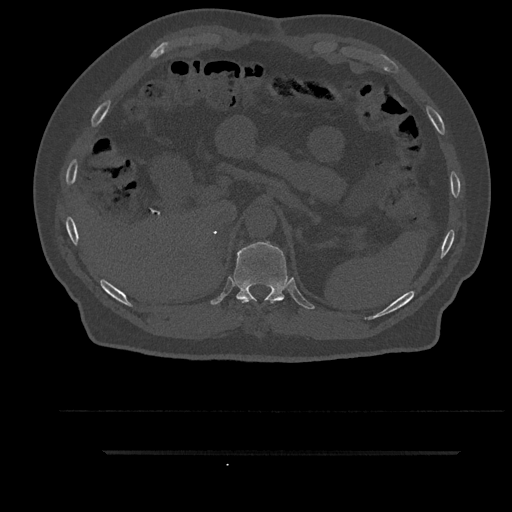
CT including the spine, one axial slice; position 326 of 797 along the scan axis; reconstruction kernel Br40s/3; 120 kVp; bone window (W 1800 / L 400 HU); 512 × 512 image matrix, field of view 432 × 432 mm. Male patient, age 63 years. From the clinical record (not read from this slice): primary cancer: renal.
Structures marked on this image (semi-automatically segmented with operator editing):
- T10 vertebra: bounding box [x1, y1, x2, y2] px = [240, 299, 274, 303]
- T11 vertebra: [234, 242, 288, 303]